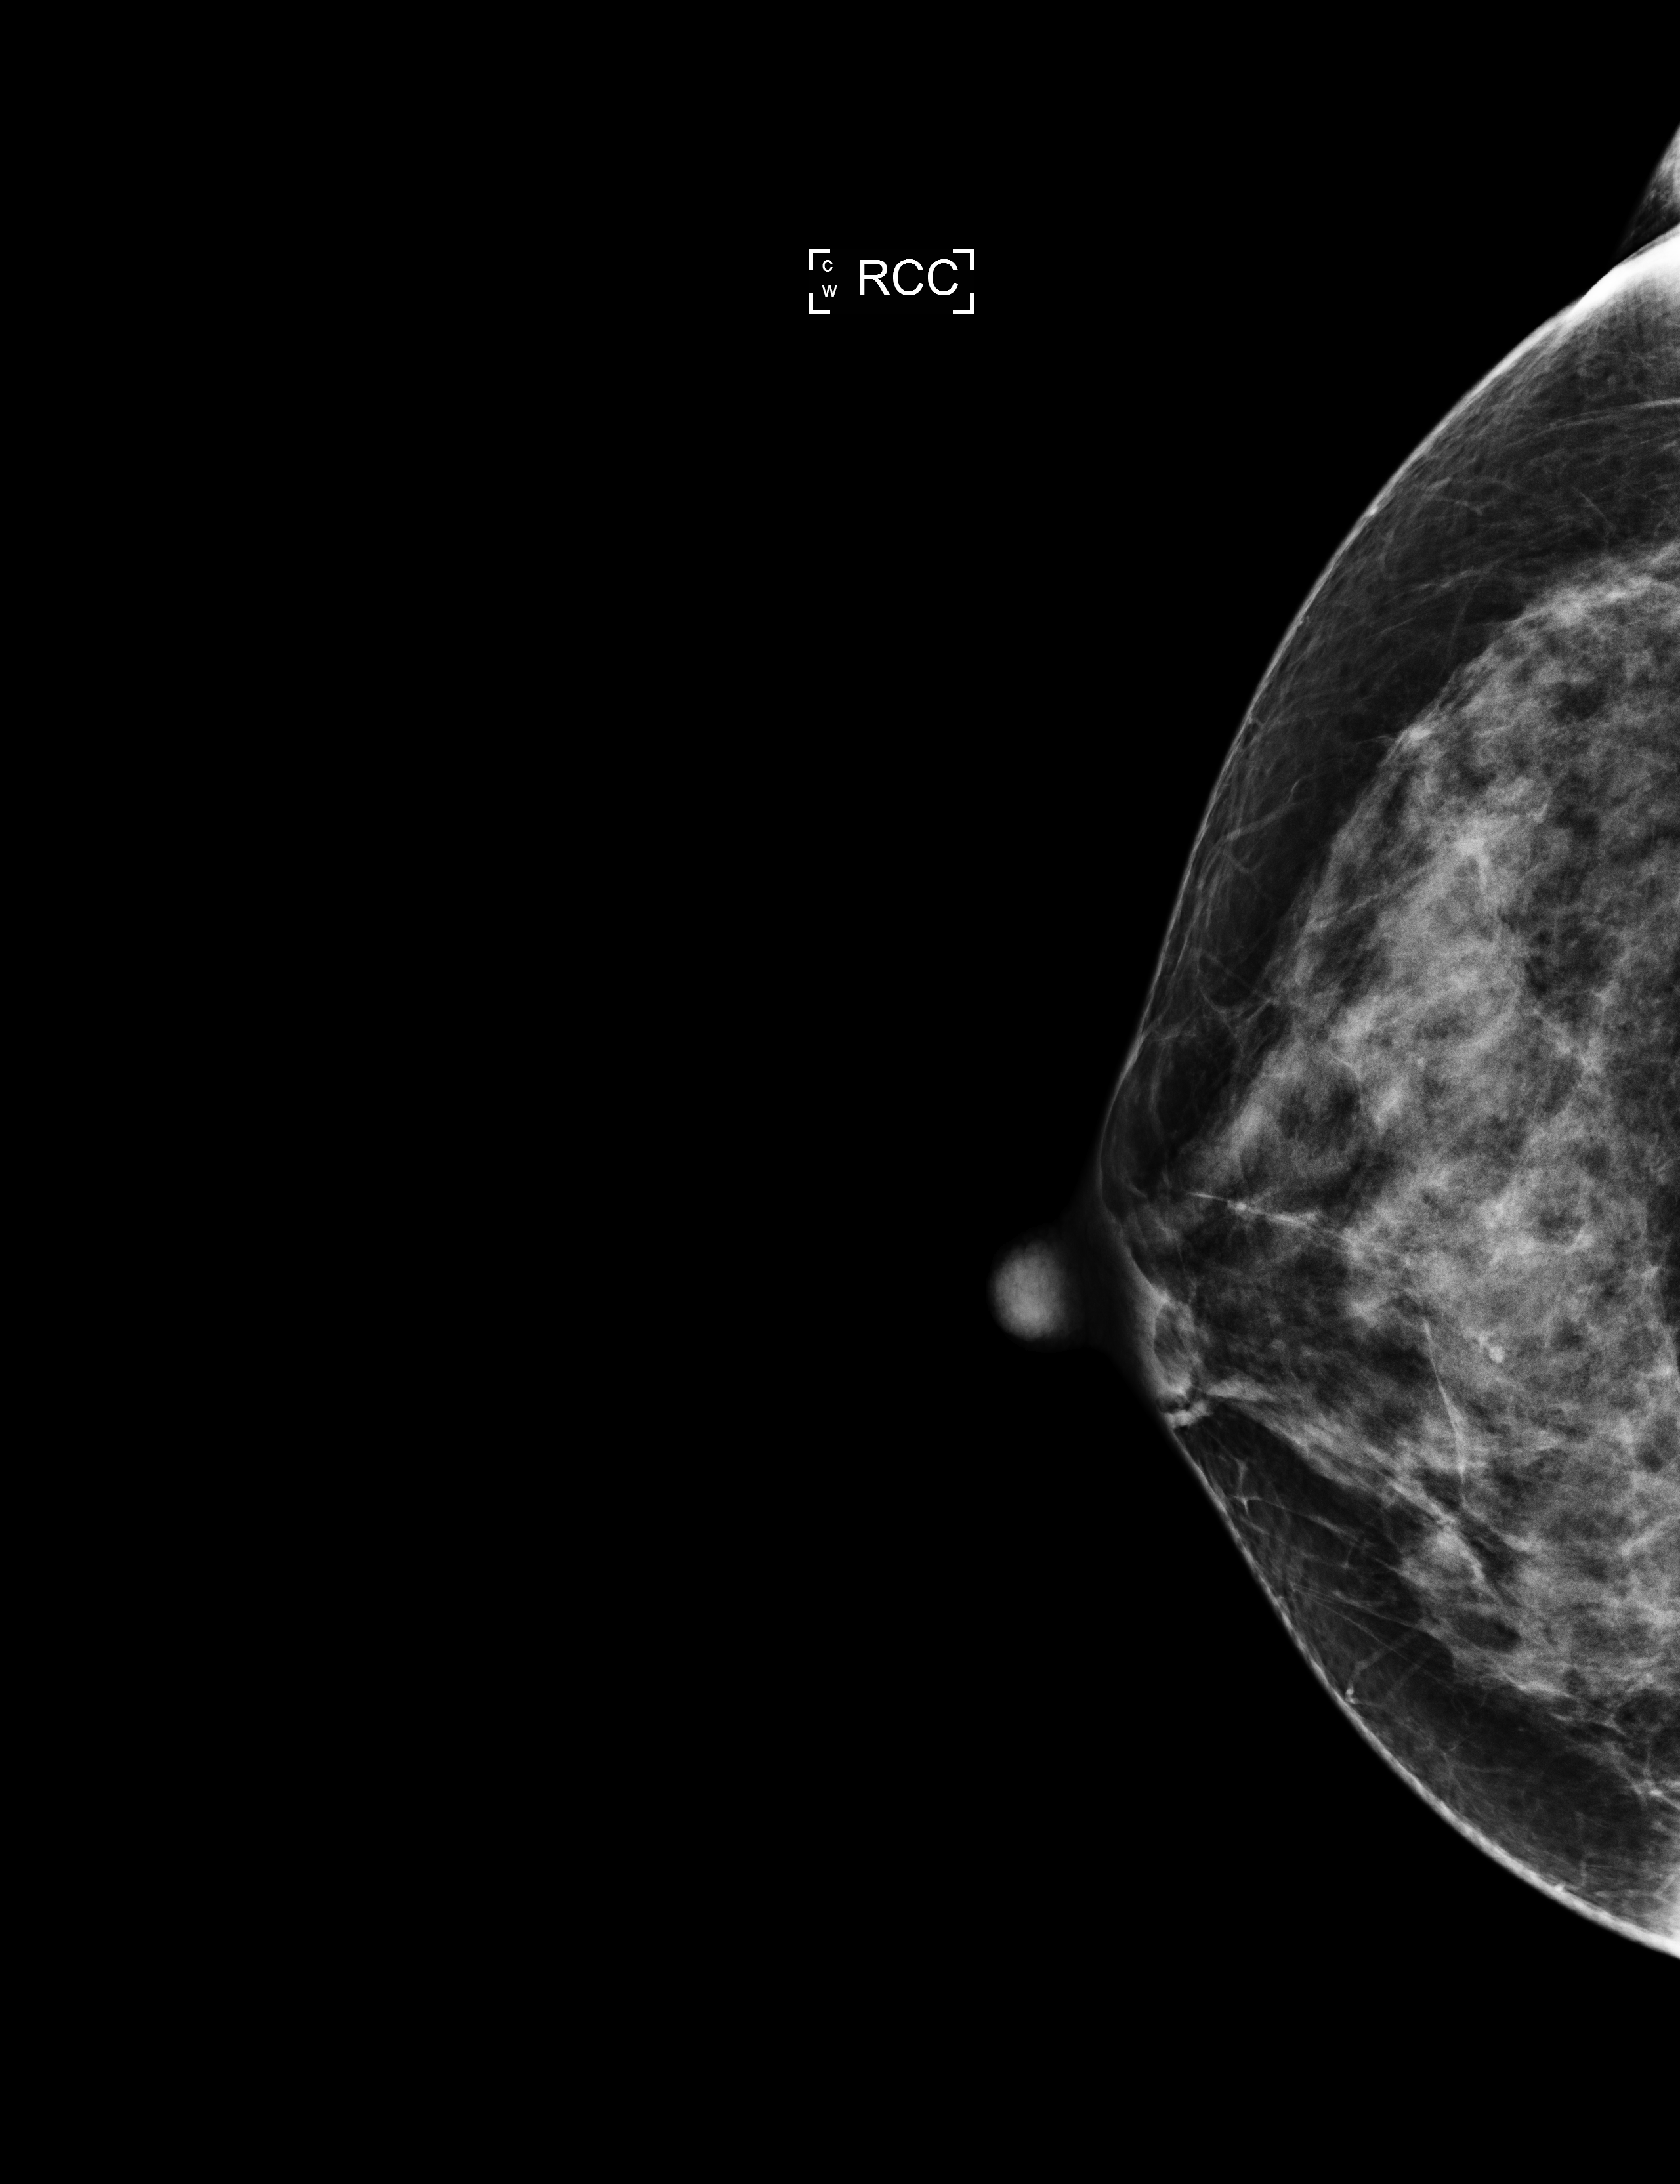
Full-field digital mammogram (FFDM), right breast, CC view, screening examination. Patient aged 41 years (female).
BI-RADS breast density category at the screening exam (both breasts, scale 1–4): 4. Final BI-RADS category for the screening round (tomosynthesis exam, both breasts): category 1. Recall: no recall after this screen.